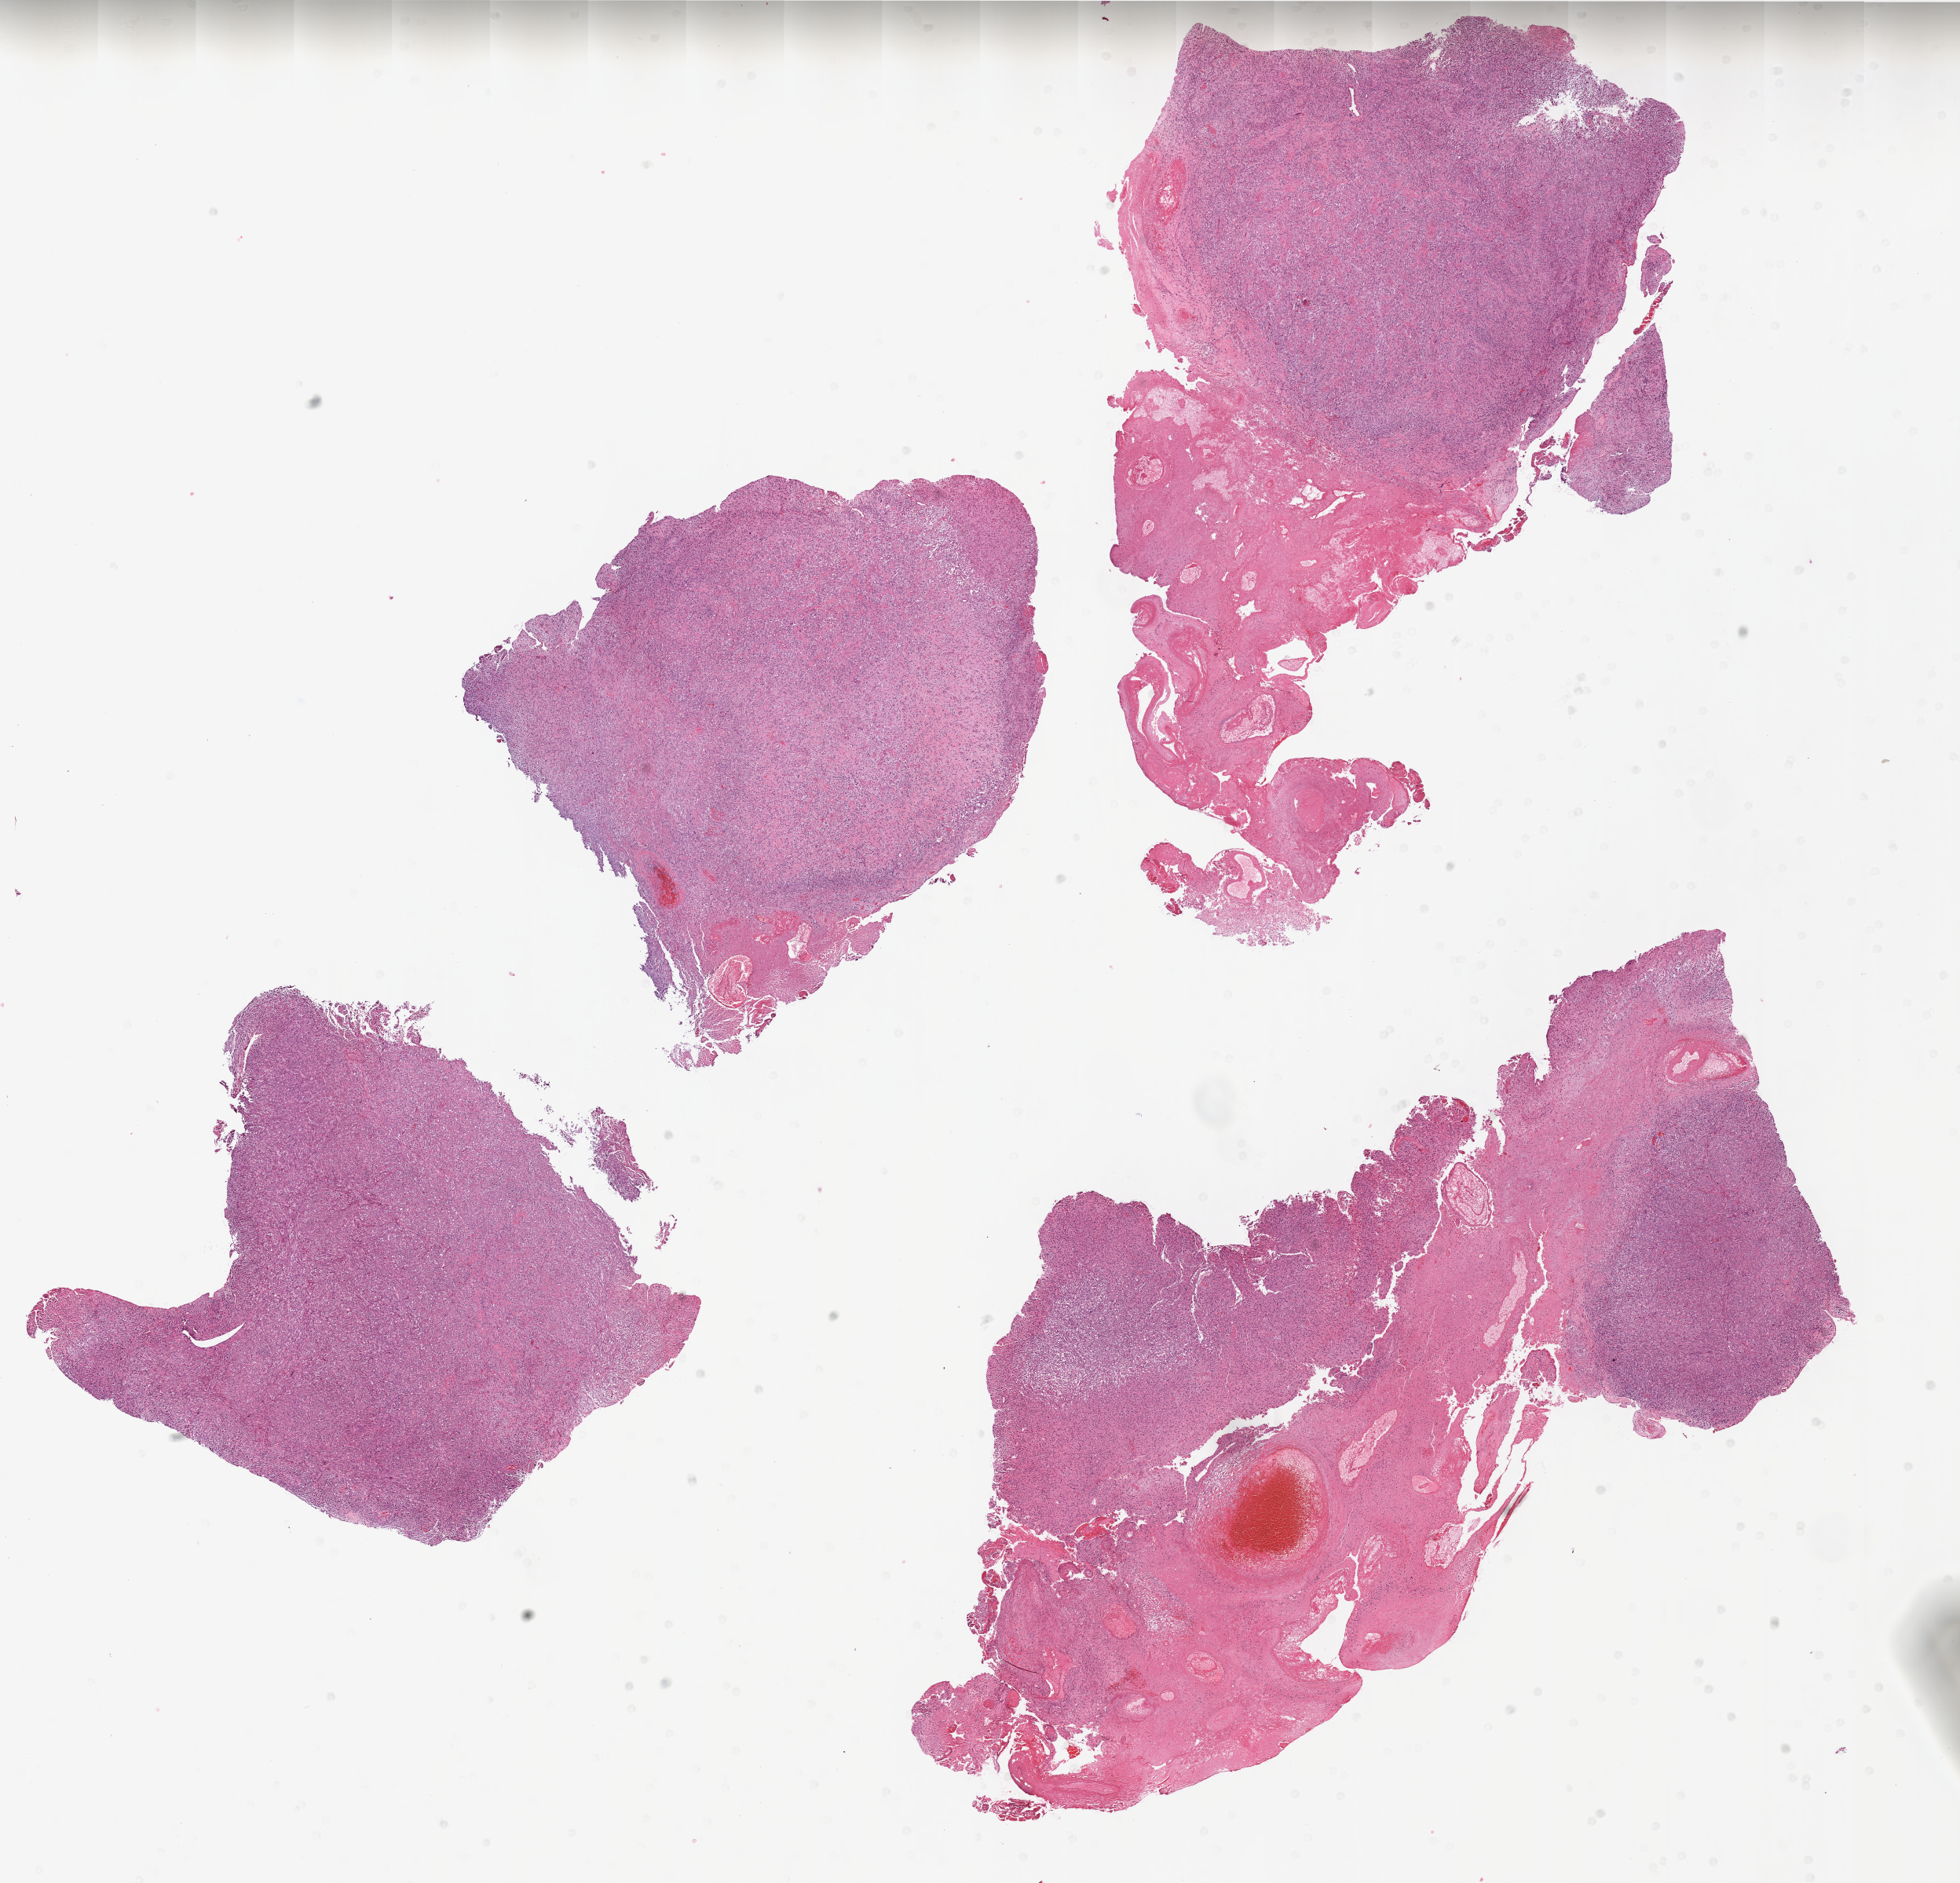
Whole-slide histology image, H&E-stained, a low-resolution overview of the entire scanned area, about 20.0 x 19.2 mm (slide scanned at 20x), formalin-fixed paraffin-embedded (FFPE) diagnostic section, primary tumour sample from the brain. Male patient; age at initial diagnosis 40 years.
Histologic diagnosis: Glioblastoma.